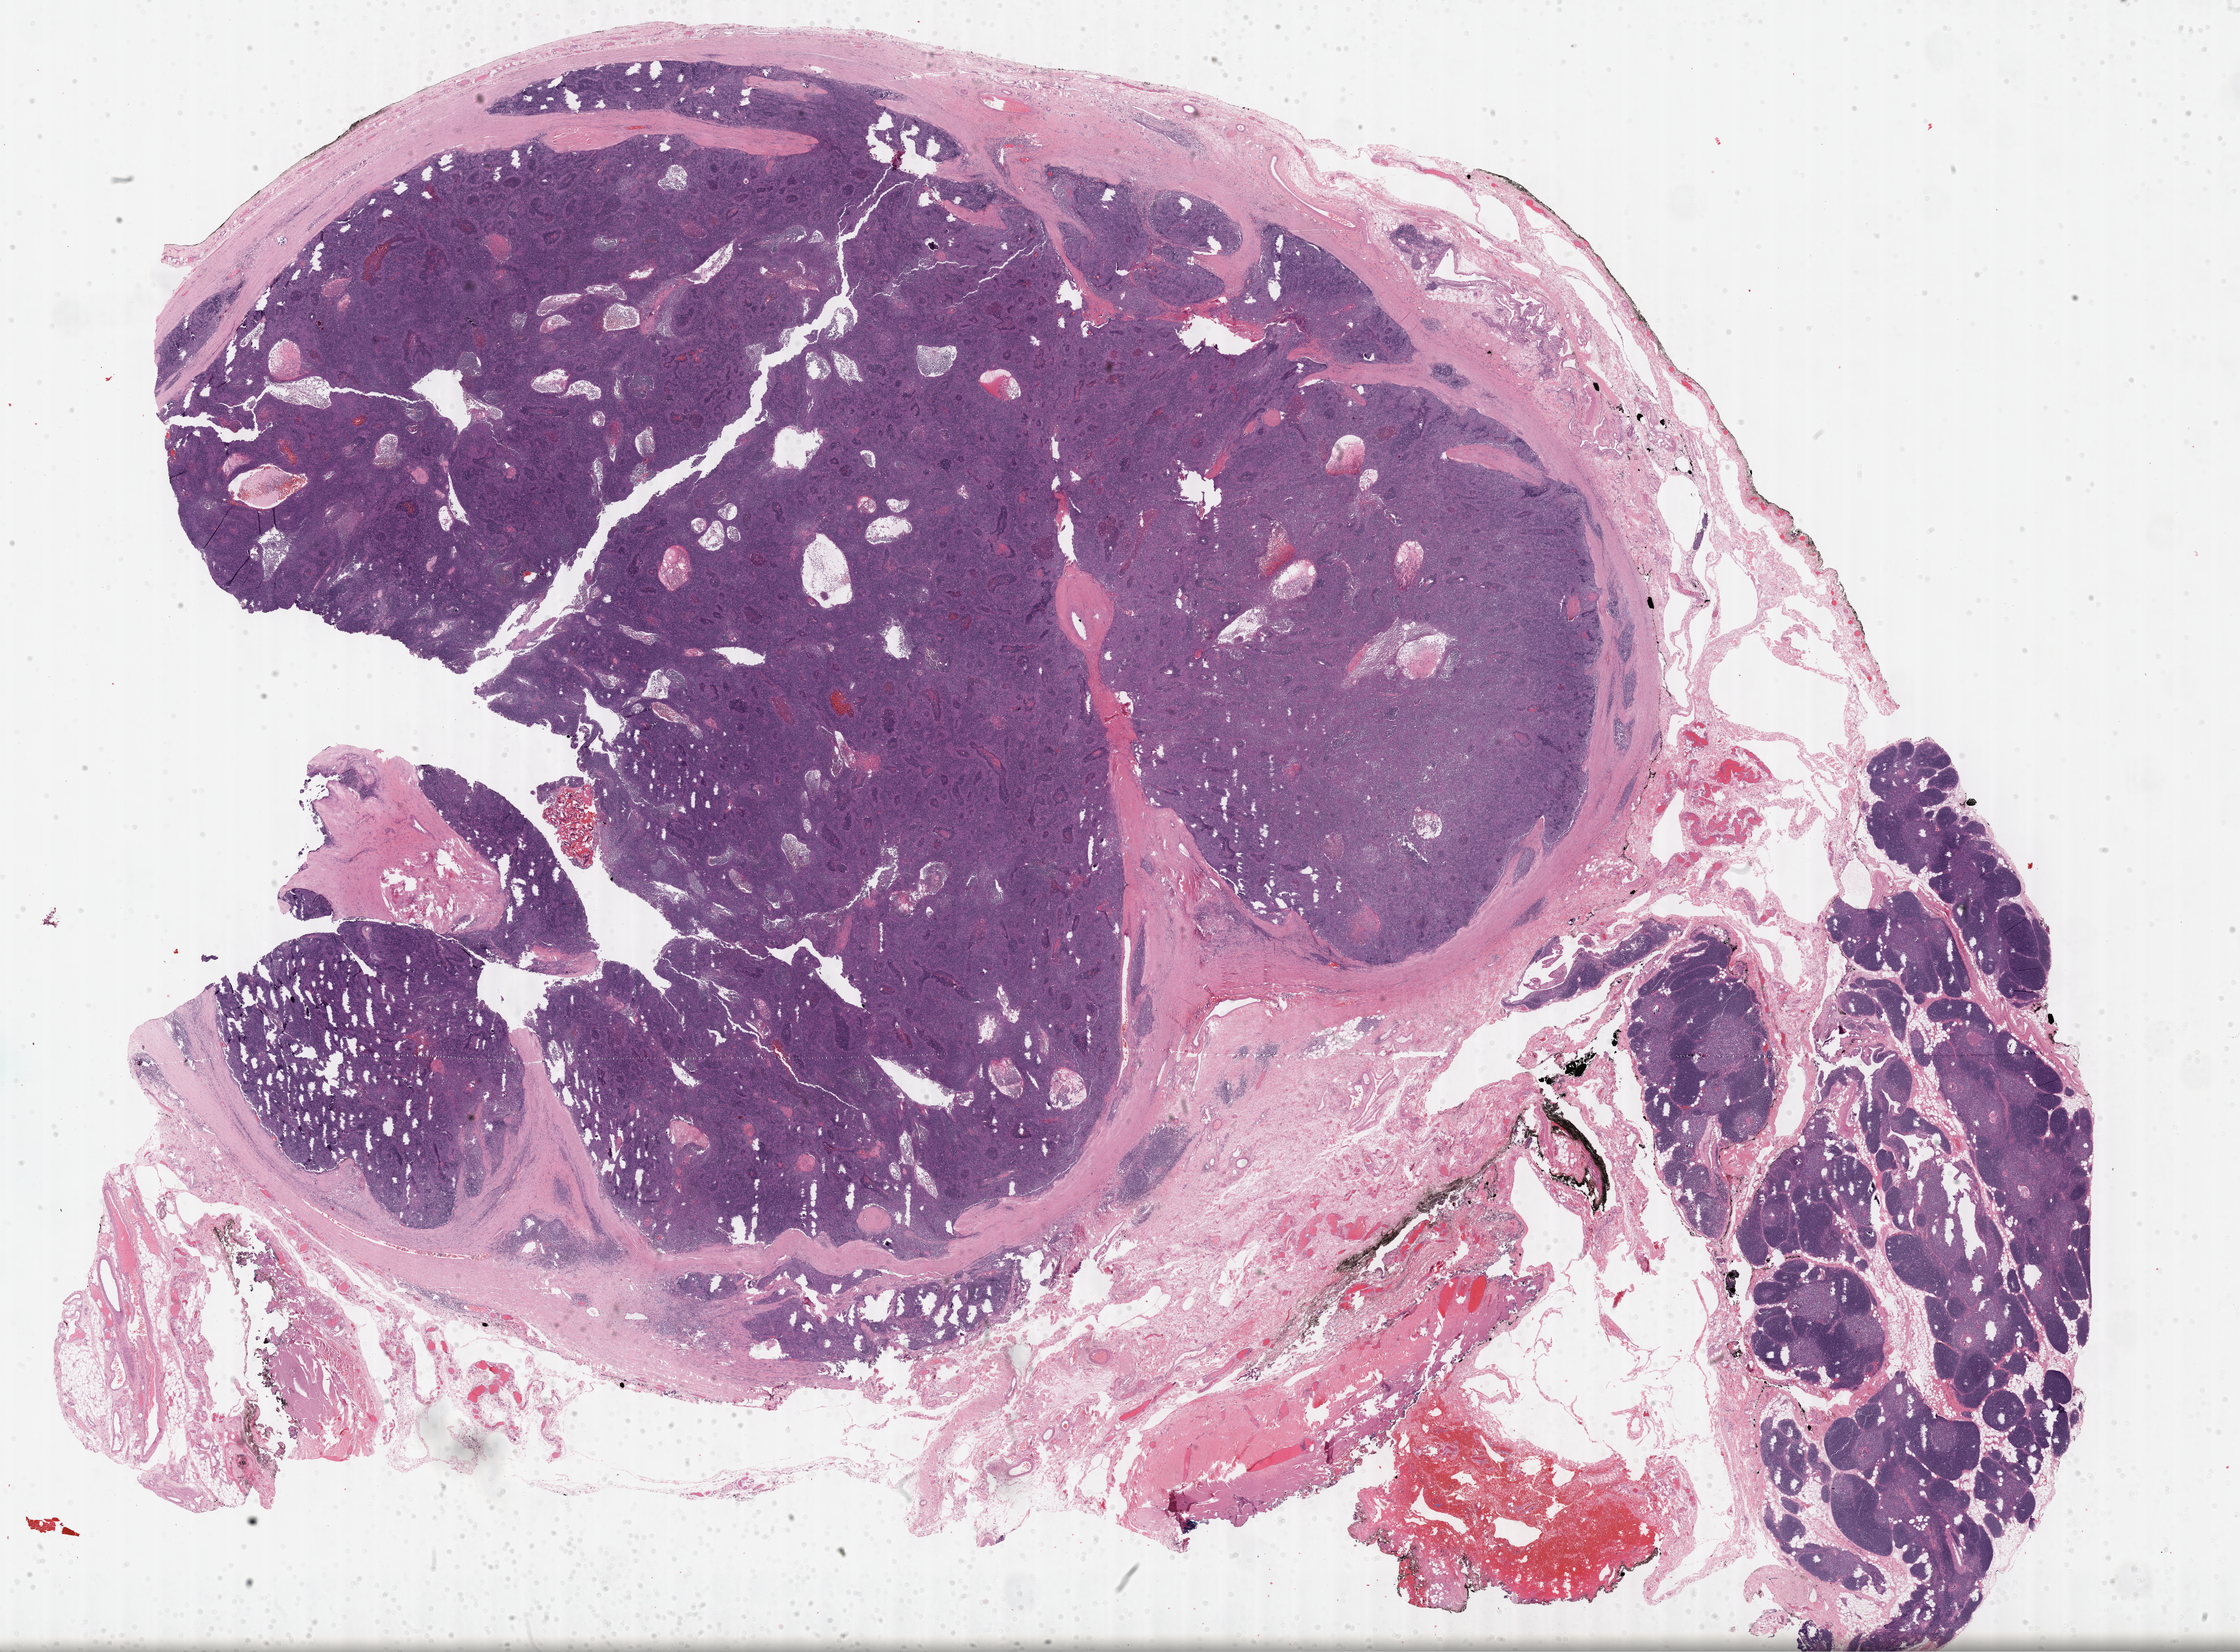
Whole-slide histology image, H&E — a low-resolution overview of the entire scanned area, about 30.7 x 22.7 mm (acquisition: 40x scan). Formalin-fixed paraffin-embedded (FFPE) diagnostic section. Primary tumour sample from the thymus. Male patient; age at initial diagnosis 26 years.
* diagnosis: Thymoma, type B2, malignant (anterior mediastinum)